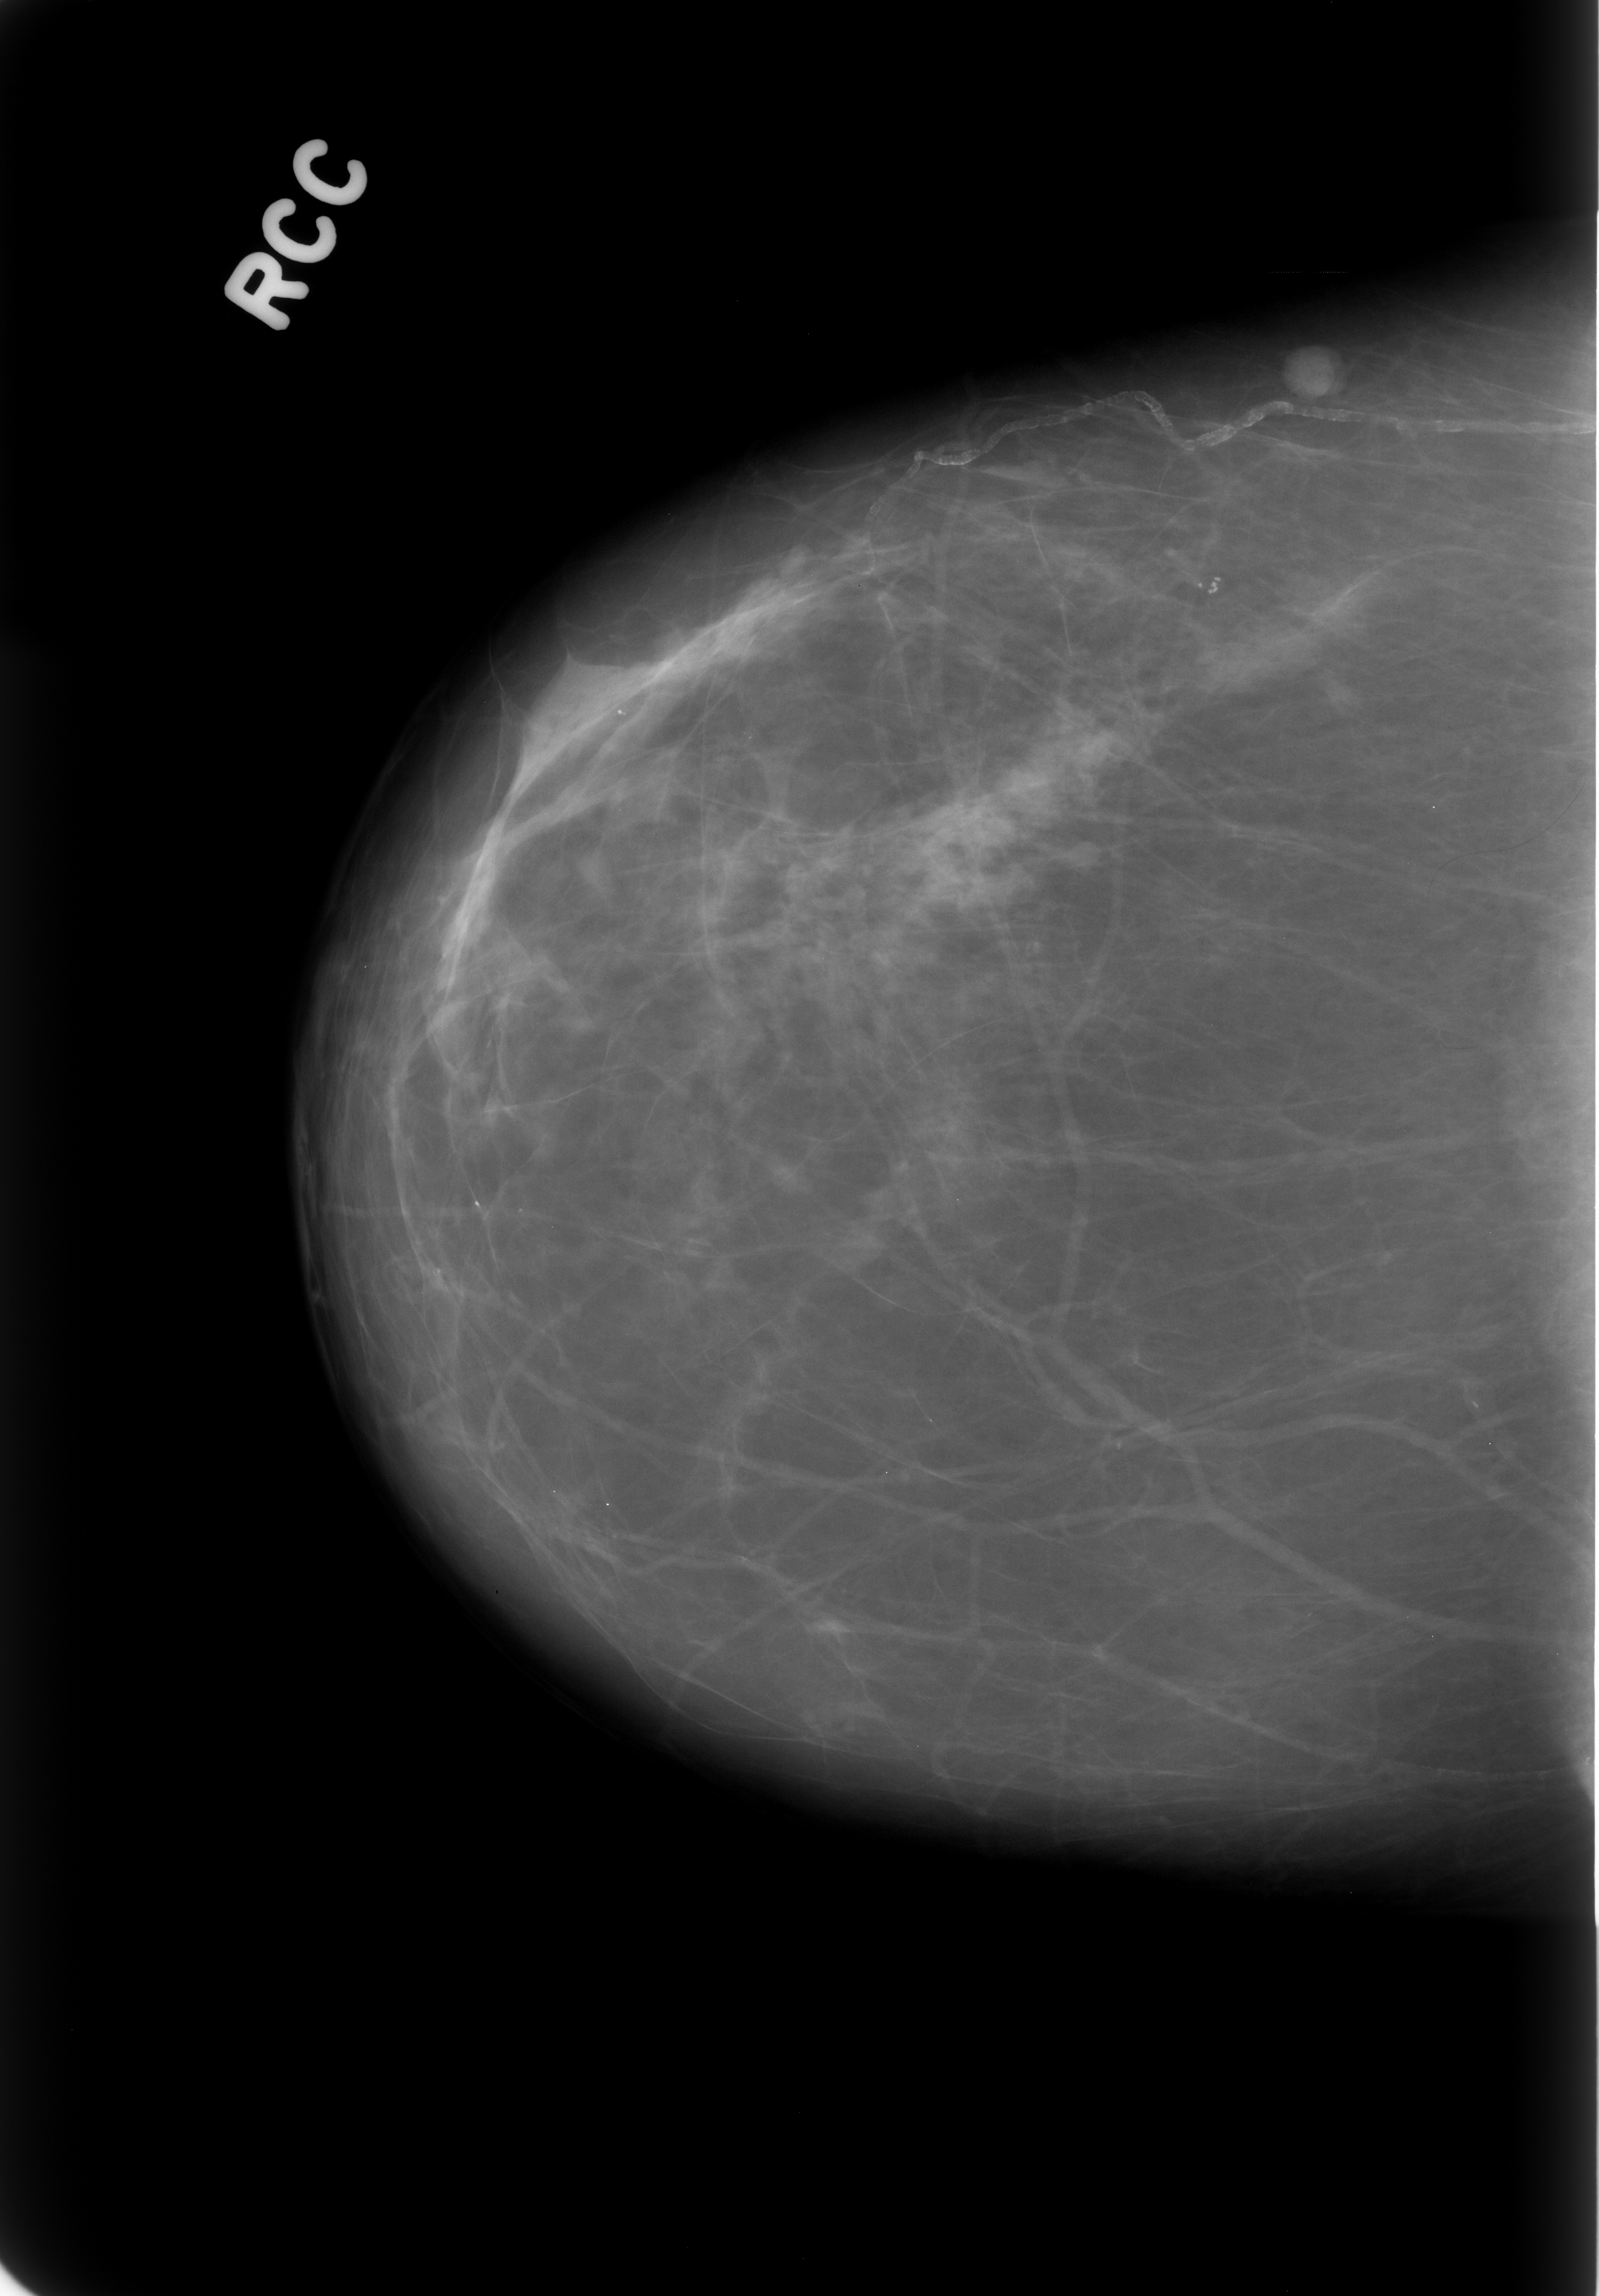
Digitized screen-film mammogram, right breast, craniocaudal (CC) view, BI-RADS breast density category 1 (scale 1–4).
Finding: mass, shape round, margins circumscribed; BI-RADS assessment category 3; subtlety rating 5 on a 1 (subtle) to 5 (obvious) scale; pathology (as recorded): benign.